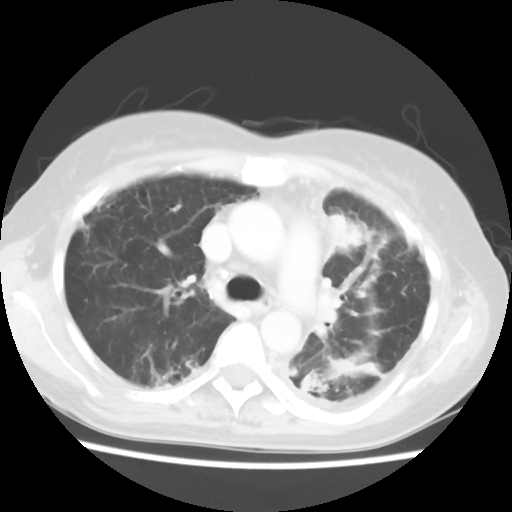
Chest CT, one axial slice; 120 kVp; lung window (W 1500 / L -600 HU); 5 mm slice thickness; 512 × 512 image matrix. Patient: female, 56 years. From the clinical record (not read from this slice): clinical TNM (as recorded): T1c N0 M1.
Structures marked on this image (bounding box drawn by a radiologist):
- lung tumour (recorded histology: adenocarcinoma): box from (x=323, y=206) to (x=367, y=260) px